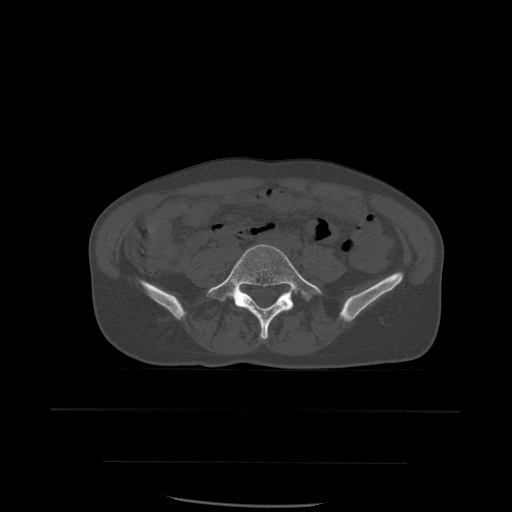
CT including the spine, one axial slice; slice 149 of 574 in the series (ordered by position); bone window (W 1800 / L 400 HU); 1.25 mm slice thickness; 512 × 512 image matrix. Patient age 48 years. From the clinical record (not read from this slice): primary cancer: lung; vertebrae with lytic lesions (as recorded): T11.
Outlined on this slice (semi-automatically segmented with operator editing):
- L5 vertebra: bounding box (x1, y1, x2, y2) in pixels: (207, 244, 323, 340)